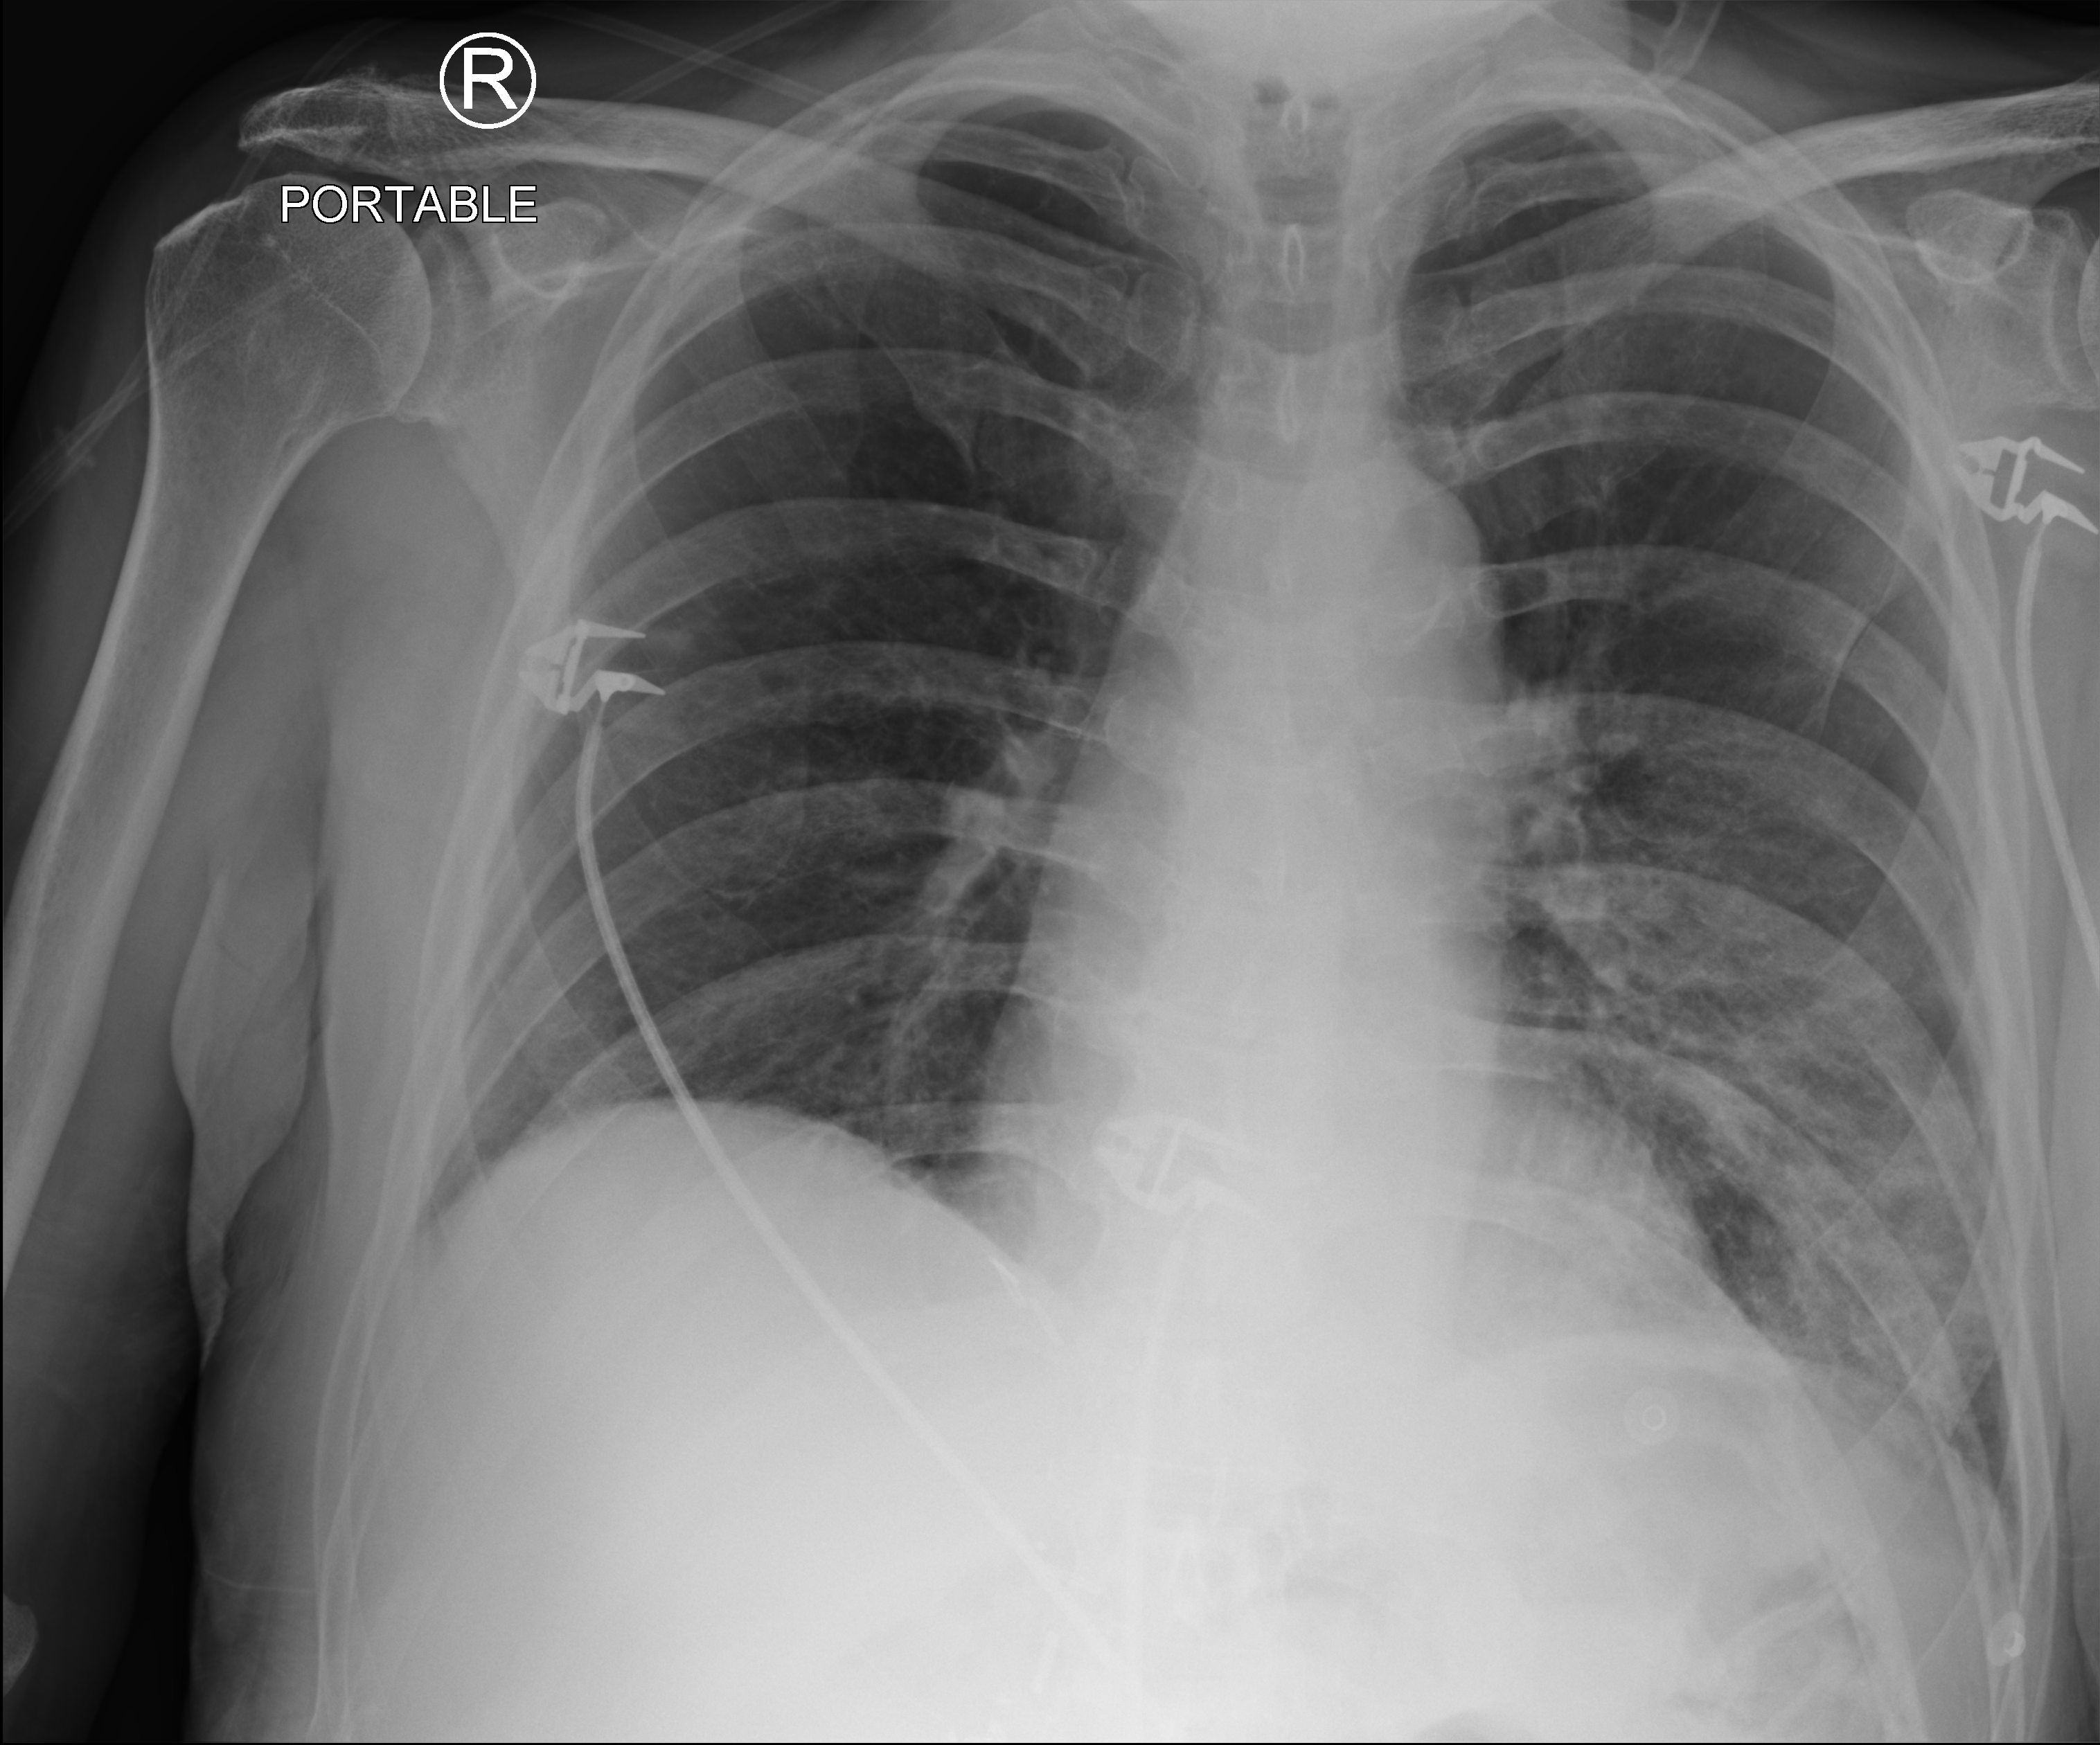
Portable chest radiograph, anteroposterior (AP) projection. Male patient hospitalised with COVID-19, age 60–74 years.
From the hospital-stay record, not from the radiograph (when in the stay this image was taken is not recorded): length of hospital stay: 4 days; smoking status (admission record): former.